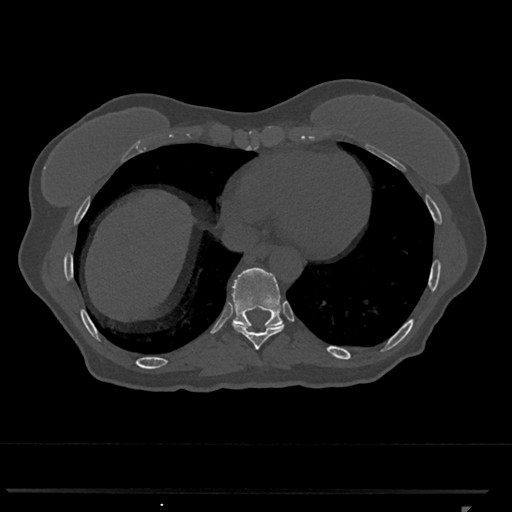
CT including the spine, one axial slice; slice 598 of 793 in the series (ordered by position); 120 kVp; bone window (W 1800 / L 400 HU); 0.5 mm slice thickness; 512 × 512 image matrix, field of view 380 × 380 mm. Patient: female, 62 years. Case-level facts recorded for this patient, not image findings: primary cancer: renal.
Annotated regions visible in this slice (semi-automatic segmentation, software-assisted and operator-edited):
- T10 vertebra: box from (x=232, y=267) to (x=283, y=327) px
- T9 vertebra: (x=233, y=323)–(x=284, y=350)